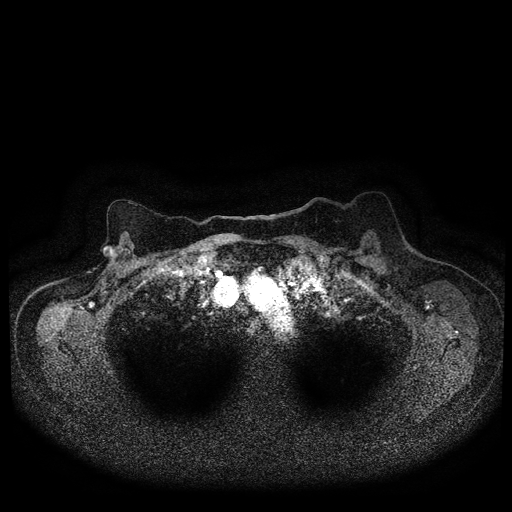
Breast MRI (dynamic contrast-enhanced, multi-phase), one axial slice; position 75 of 116 along the scan axis; dynamic contrast-enhanced series, time point 2 of 5 at this slice position (early post-contrast); 1.5 T; TE 2.7 ms, TR 5.4 ms; 512 × 512 image matrix, field of view 340 × 340 mm. Female patient, age 72 years.
Annotated regions visible in this slice (semi-automatically segmented with operator editing):
- breast lesion (labelled 'tumour' in the annotation; benign lesions carry a separate 'benign' label): bounding box [x1, y1, x2, y2] px = [101, 245, 117, 260]